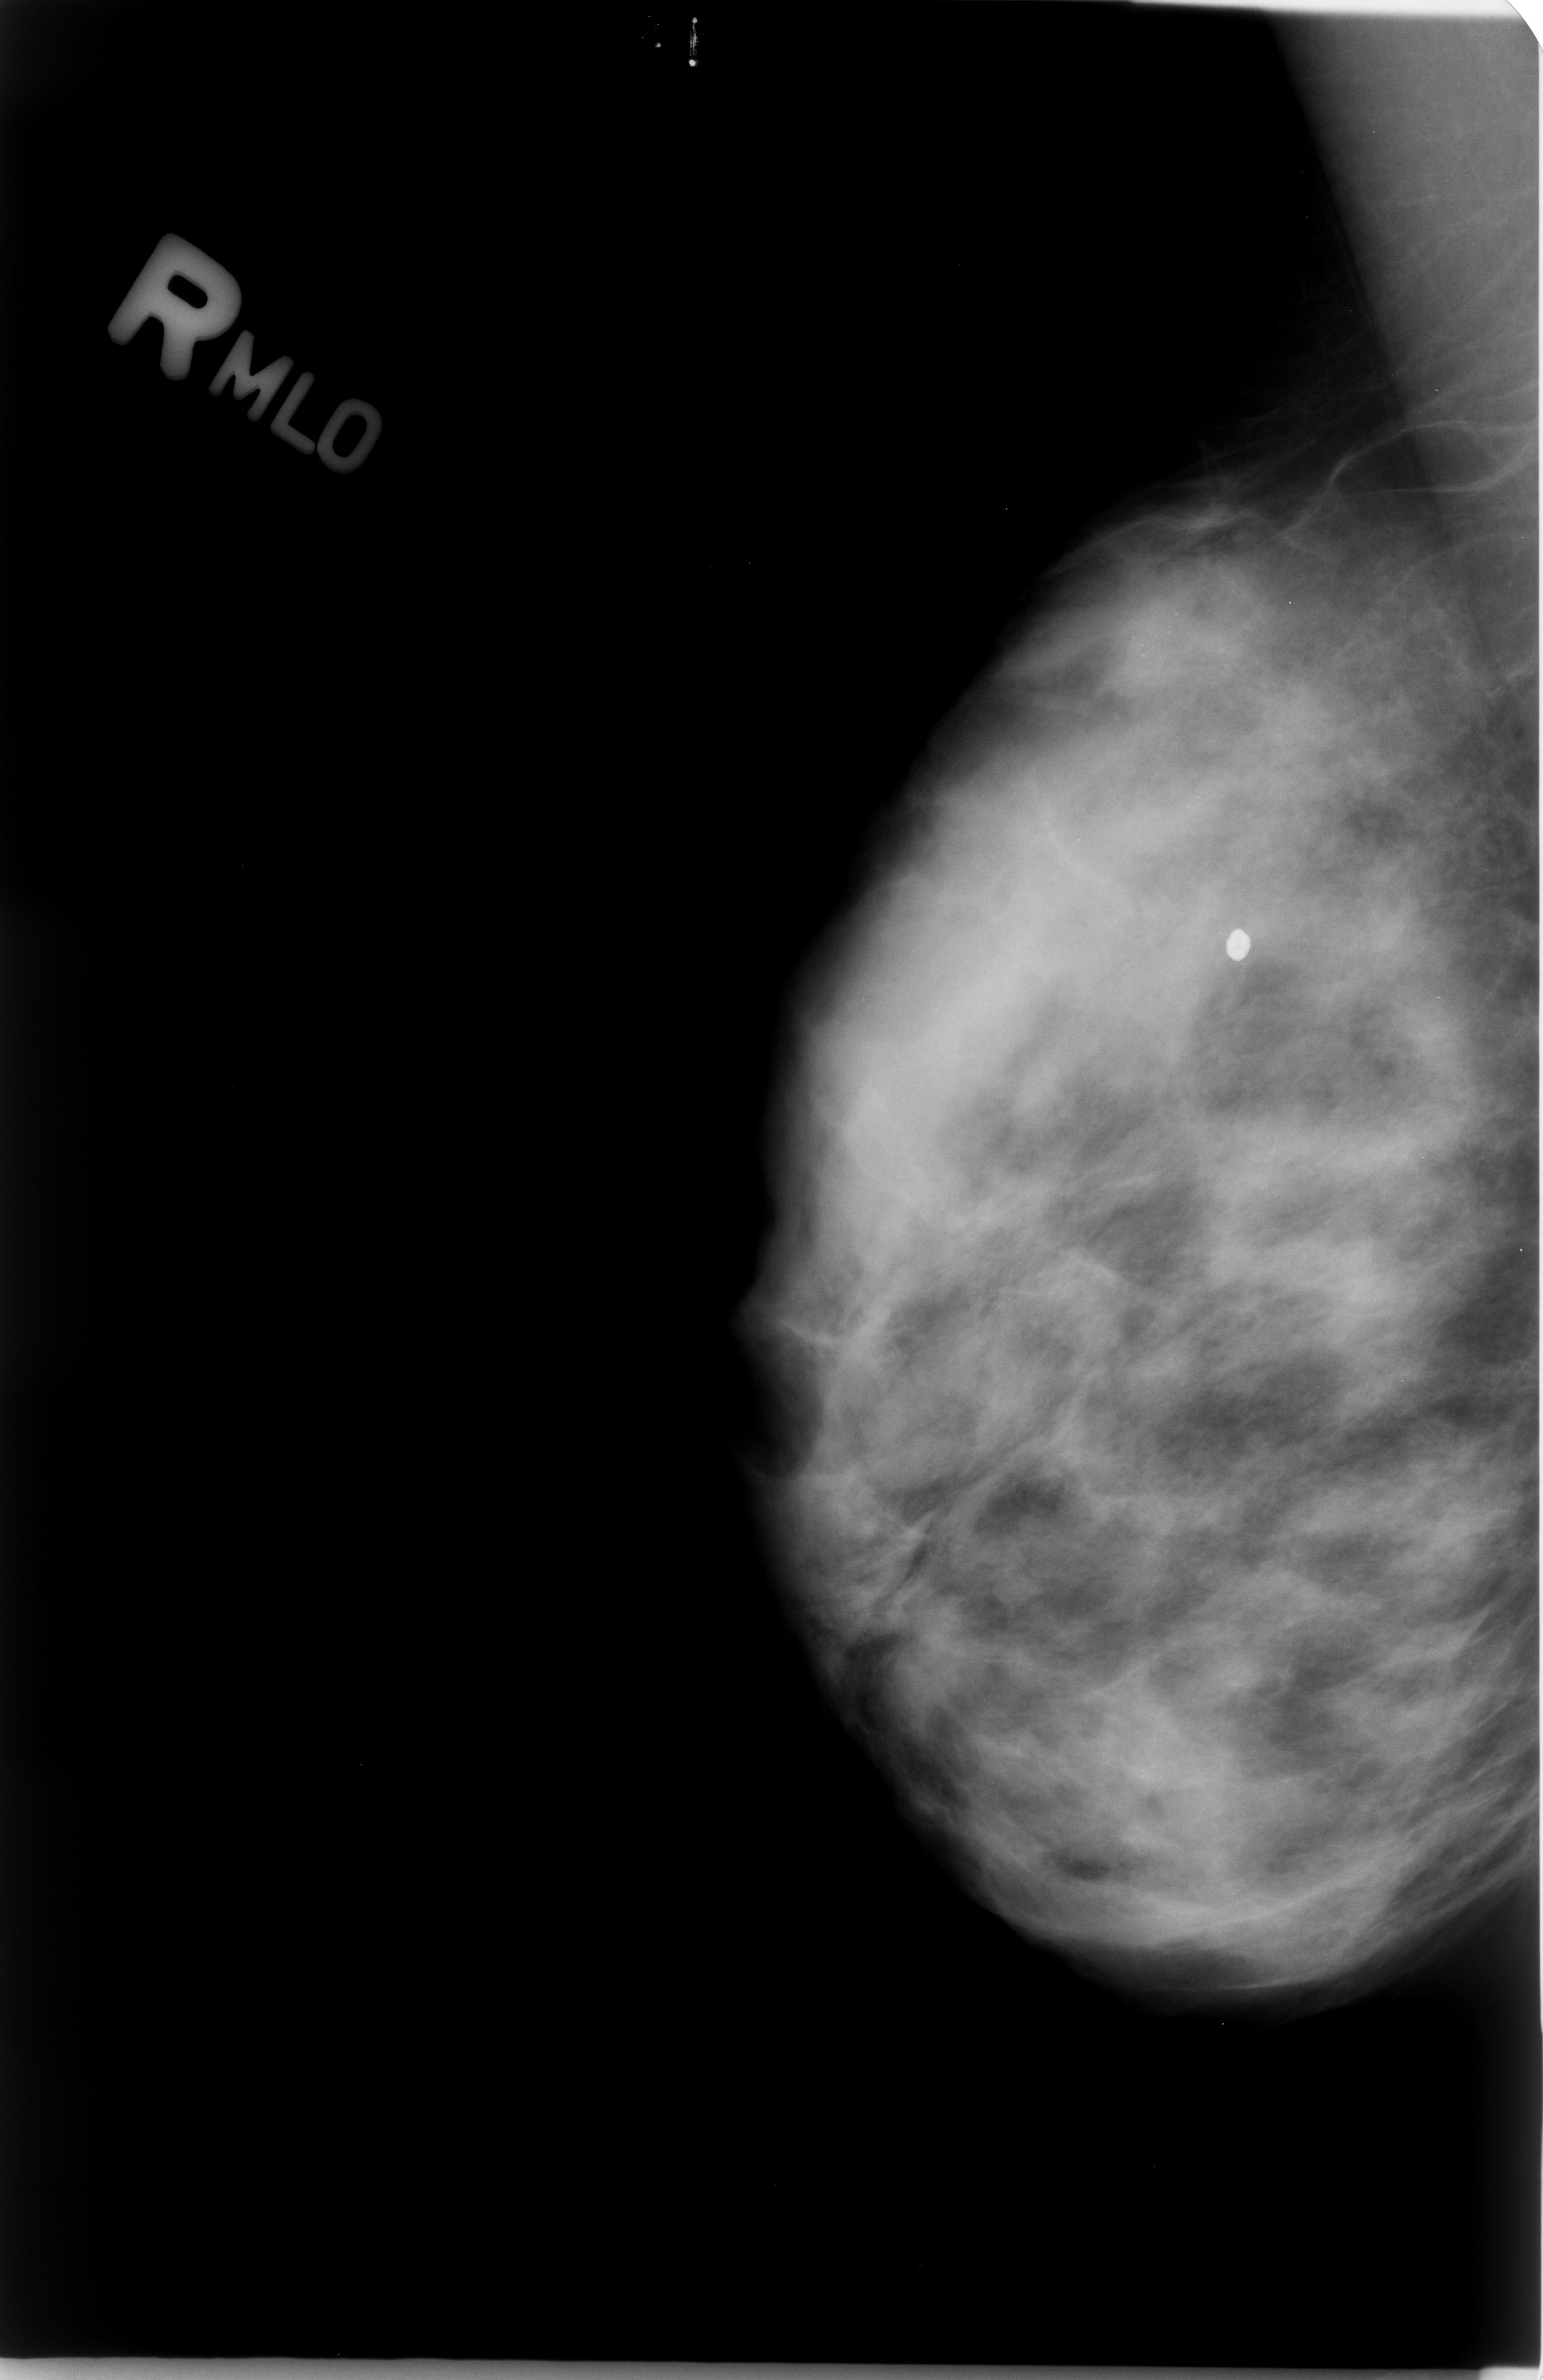
Scanned film-screen mammogram, right breast, mediolateral oblique (MLO) view, BI-RADS breast density category 3 (scale 1–4).
Marked abnormality: calcifications, morphology punctate, distribution clustered; BI-RADS assessment category 4; subtlety rating 3 on a 1 (subtle) to 5 (obvious) scale; pathology (as recorded): benign.